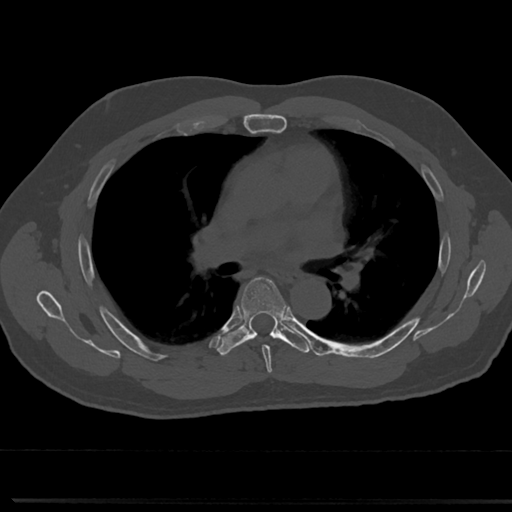
CT including the spine, one axial slice. Slice 468 of 817 in the series (ordered by position). Bone window (W 1800 / L 400 HU). 512 × 512 image matrix, field of view 355 × 355 mm. Male patient, age 61 years. From the clinical record (not read from this slice): primary cancer: prostate.
Annotated regions visible in this slice (semi-automatically segmented with operator editing):
- T5 vertebra: bounding box <242,278,284,363> (left, top, right, bottom; pixels)
- T6 vertebra: <218,275,305,354>